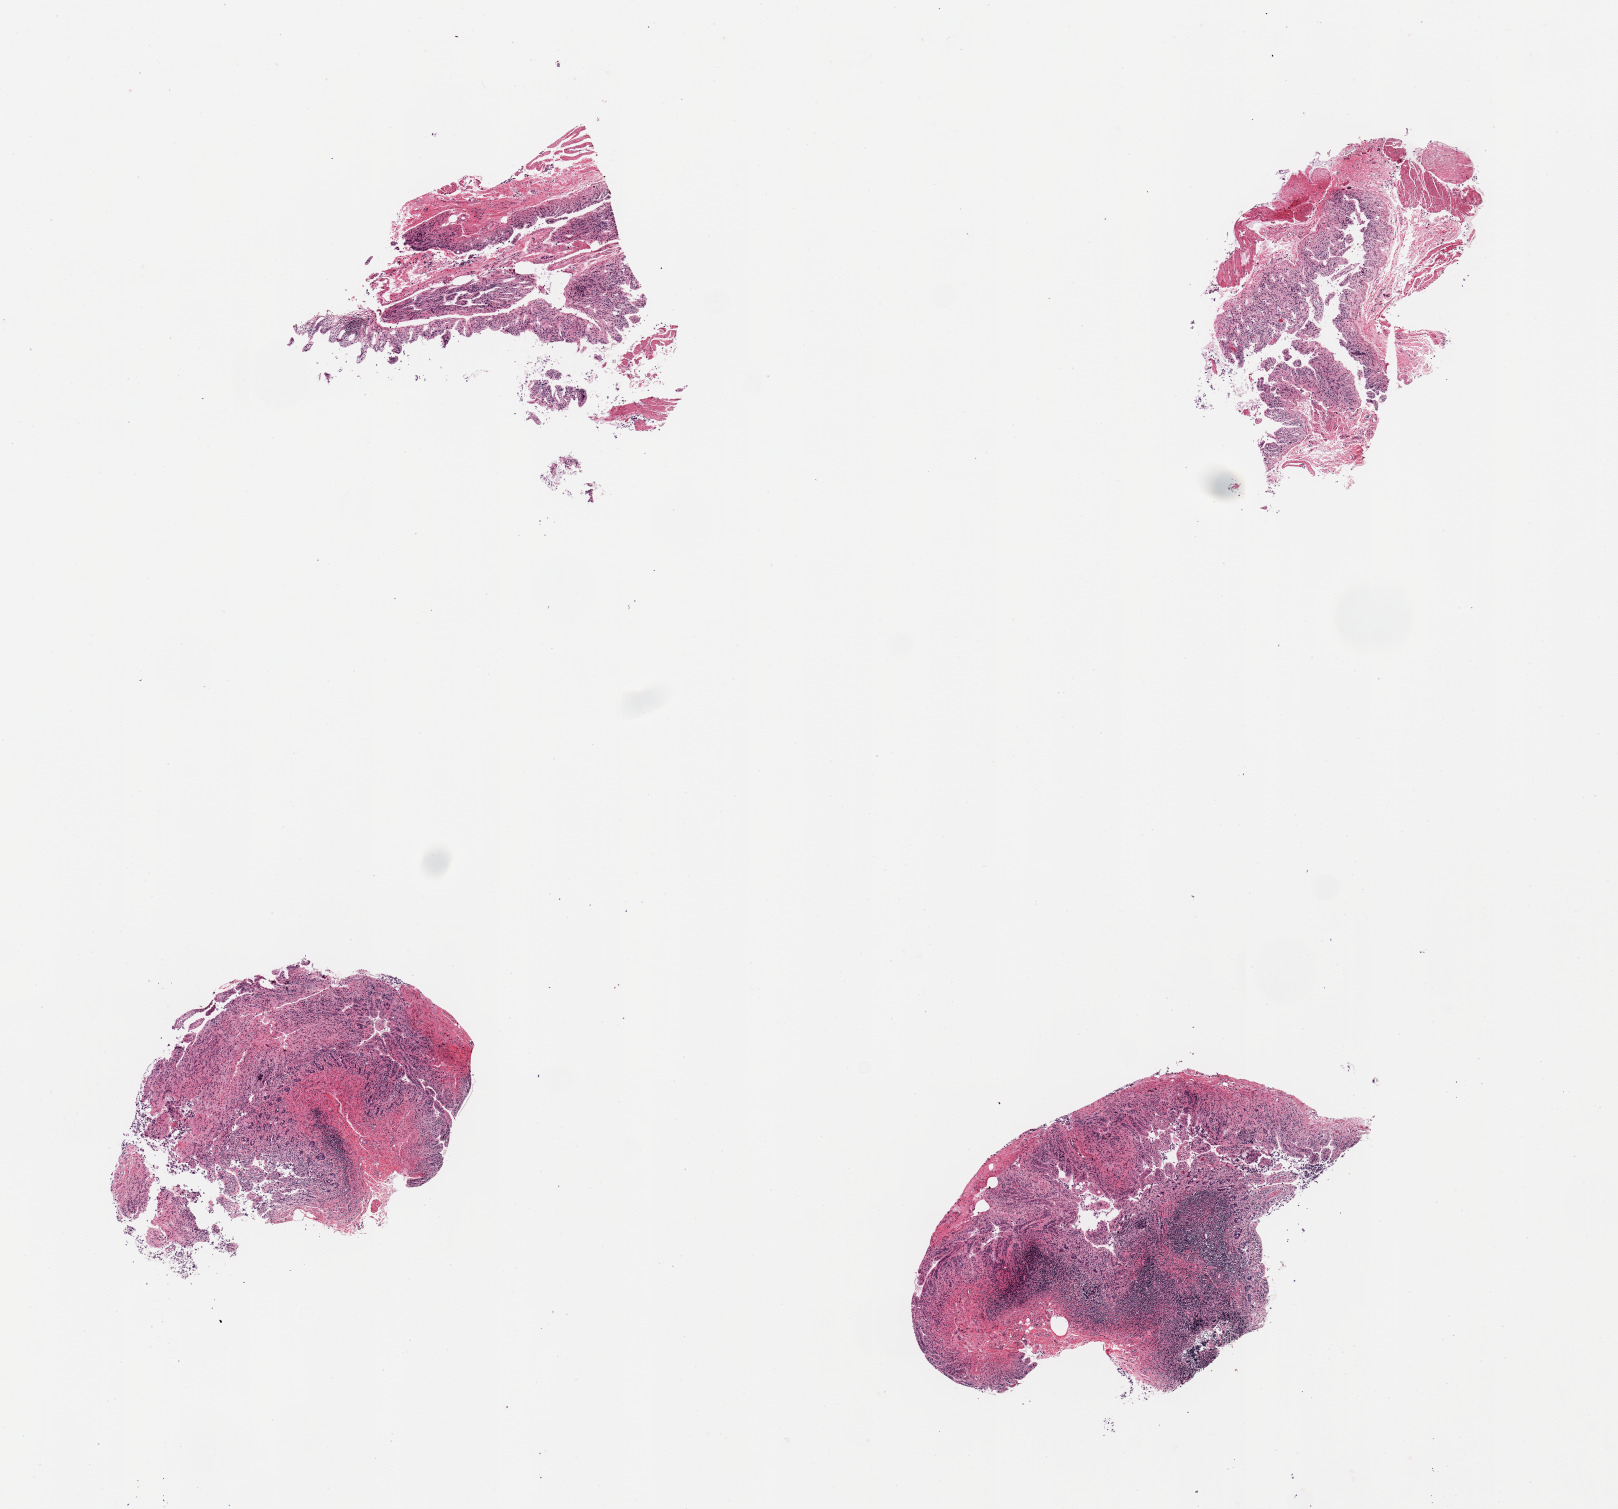
Digitized H&E-stained section, brightfield, whole scanned area (about 12.8 x 11.9 mm, from a 20x scan) shown as a low-resolution overview. Female donor.
• specimen: PAXgene-fixed paraffin-embedded (PFPE) section; section of ileum (target tissue); donor tissue sample